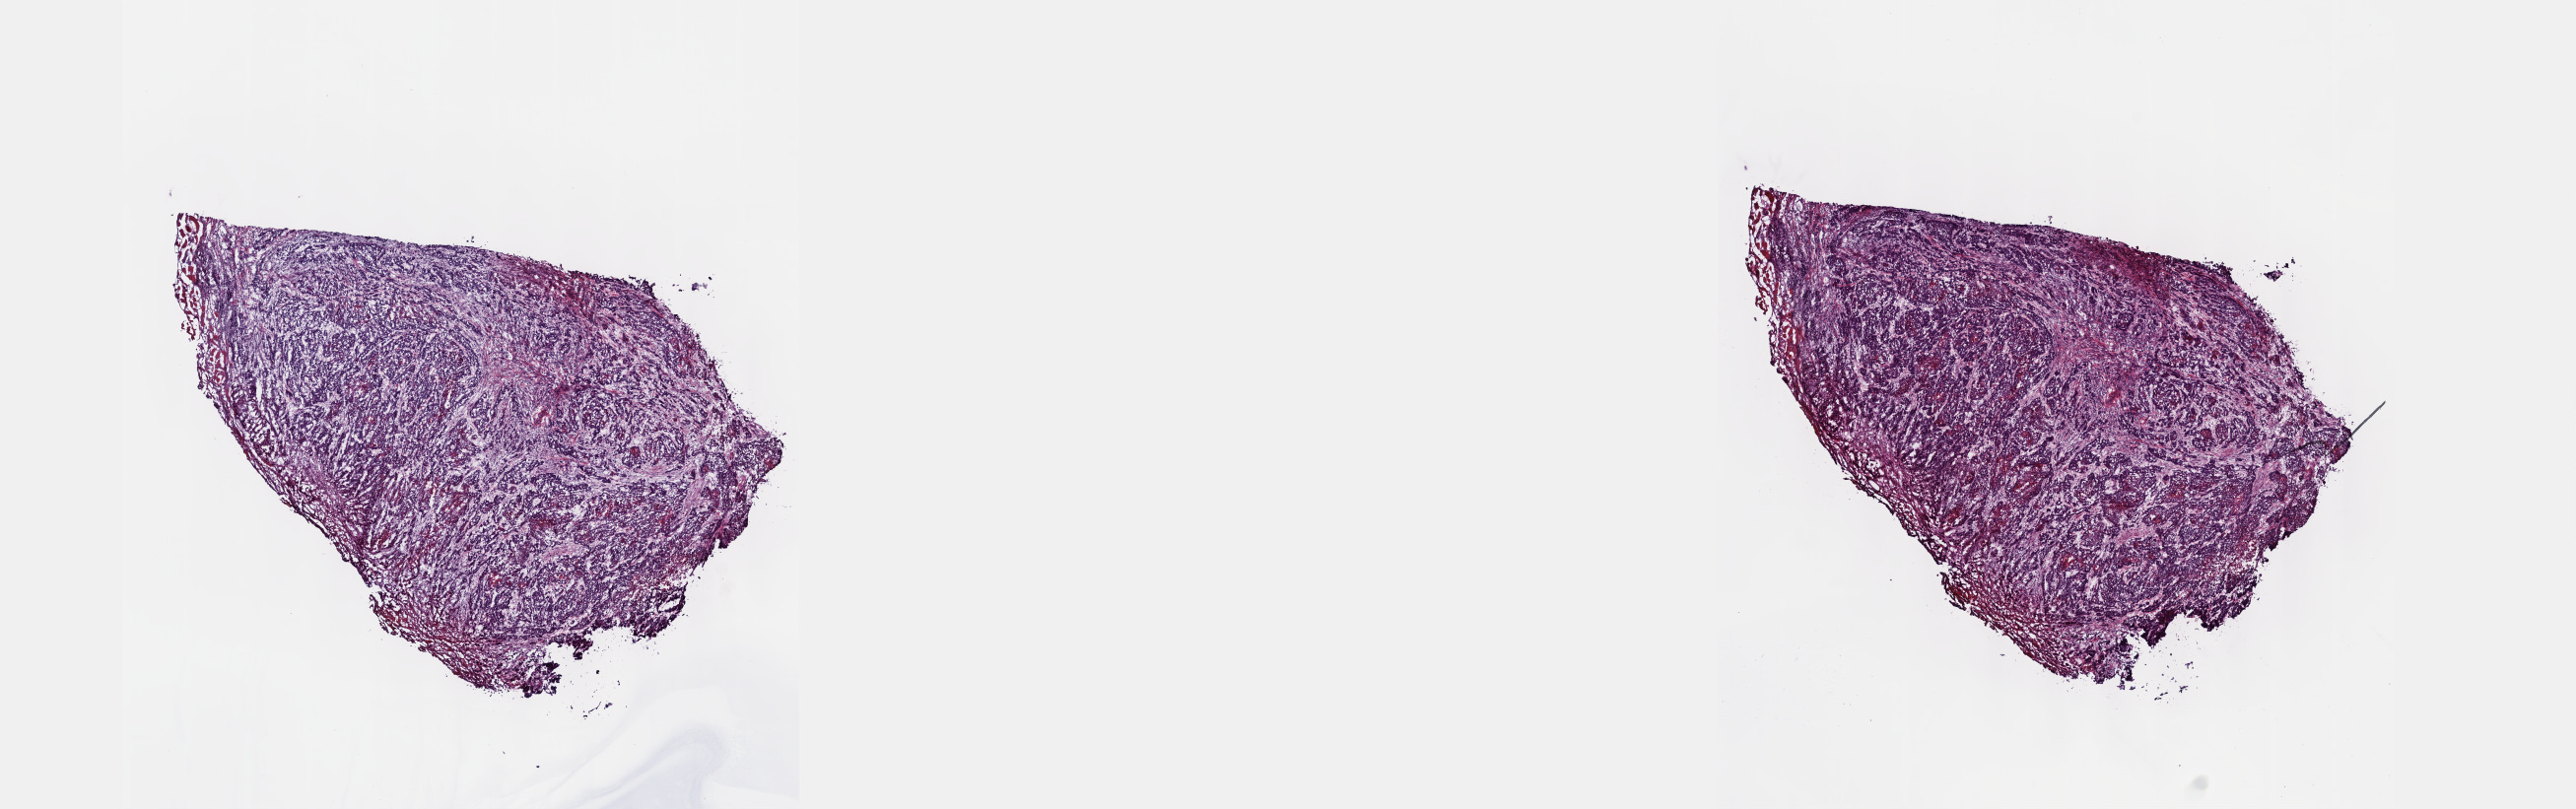
Whole-slide histology image, Hematoxylin and eosin (H&E) stained — whole scanned area (about 21.1 x 6.6 mm) shown as a low-resolution overview. Frozen section from the top of the tissue portion. Primary tumour sample from the head and neck. Male patient; age at initial diagnosis 79 years. Histologic grade: G3 (poorly differentiated). Pathologist review of this section (percent, as recorded): tumour cells 90%, tumour nuclei 90%, normal cells 0%, stromal cells 10%, necrosis 0%. Inflammatory infiltration, as recorded: lymphocyte infiltration 5%, monocyte infiltration 0%, neutrophil infiltration 0%.
AJCC pathologic stage: IVA (7th edition). Pathologic diagnosis: Squamous cell carcinoma, NOS. TNM: T2 N2c MX.